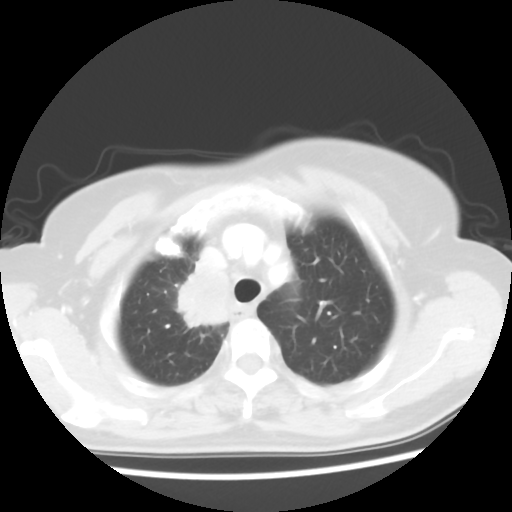
Chest CT, one axial slice. Slice 46 of 56 in the series (ordered by position). Reconstruction kernel STANDARD. Lung window (W 1500 / L -600 HU). 5 mm slice thickness. 512 × 512 image matrix, field of view 314 × 314 mm. Female patient, age 62 years. Case-level facts recorded for this patient, not image findings: clinical TNM (as recorded): T2 N1 M1a.
Structures marked on this image (bounding box drawn by a radiologist):
- lung tumour (recorded histology: adenocarcinoma): box from (x=166, y=257) to (x=238, y=333) px